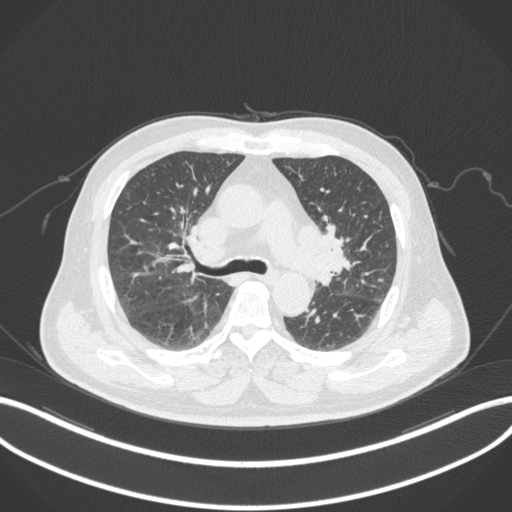
Chest CT, one axial slice; slice 187 of 286 in the series (ordered by position); reconstruction kernel B31f; lung window (W 1500 / L -600 HU); 512 × 512 image matrix, field of view 400 × 400 mm. Male patient, age 67 years. Case-level facts recorded for this patient, not image findings: clinical TNM (as recorded): T2a N1 M0.
Structures marked on this image (bounding box drawn by a radiologist):
- lung tumour (recorded histology: adenocarcinoma): bounding box [x1, y1, x2, y2] px = [318, 223, 348, 278]